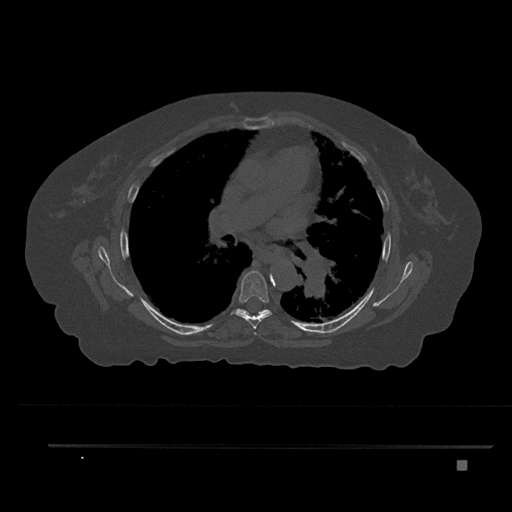
CT including the spine, one axial slice; slice 521 of 797 in the series (ordered by position); 120 kVp; bone window (W 1800 / L 400 HU); 0.5 mm slice thickness; 512 × 512 image matrix, field of view 437 × 437 mm. Patient: female, 76 years. From the clinical record (not read from this slice): primary cancer: lung; vertebrae with lytic lesions (as recorded): T11, L3.
Outlined on this slice (semi-automatic segmentation, software-assisted and operator-edited):
- T5 vertebra: bounding box [x1, y1, x2, y2] px = [254, 332, 257, 335]
- T6 vertebra: [235, 271, 272, 329]
- T7 vertebra: [236, 309, 270, 316]